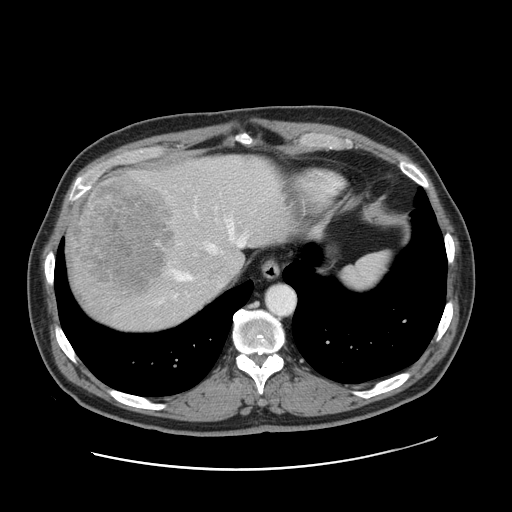
Contrast-enhanced abdominal CT, one axial slice; slice 134 of 178 in the series (ordered by position); intravenous contrast given; soft-tissue window (W 400 / L 40 HU); 2.5 mm slice thickness; 512 × 512 image matrix. Male patient, age 63 years. From the clinical record (not read from this slice): diagnosis: colorectal cancer liver metastases, imaged before liver resection; multiple liver metastases: yes.
Annotated regions visible in this slice (outlined manually by an expert reader):
- hepatic veins: bounding box (x1, y1, x2, y2) in pixels: (175, 211, 246, 280)
- liver: (66, 155, 293, 331)
- planned liver remnant (the part of the liver to remain after resection): (164, 158, 293, 281)
- portal vein (with intrahepatic branches): (157, 242, 159, 244)
- liver metastasis: (68, 175, 176, 297)